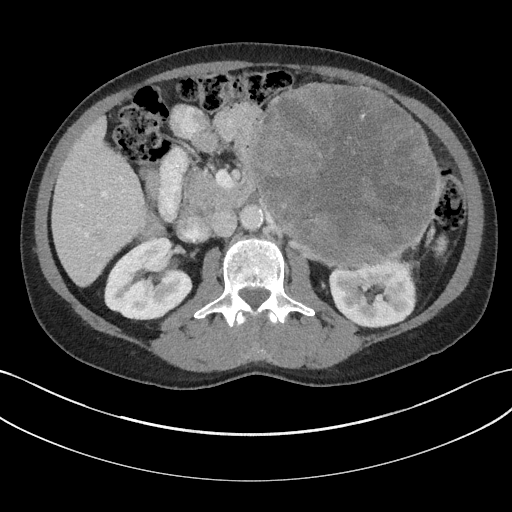
Contrast-enhanced abdominal CT, one axial slice. Reconstruction kernel I31f/3. Intravenous contrast given. Soft-tissue window (W 400 / L 40 HU). 3 mm slice thickness. 512 × 512 image matrix, field of view 384 × 384 mm. Patient: male, 58 years. Case-level facts recorded for this patient, not image findings: diagnosis: adrenocortical carcinoma; tumour side: left adrenal; tumour size at pathology: 22 cm.
Annotated regions visible in this slice (semi-automatic segmentation, software-assisted and operator-edited):
- mass: bounding box (x1, y1, x2, y2) in pixels: (254, 85, 437, 264)